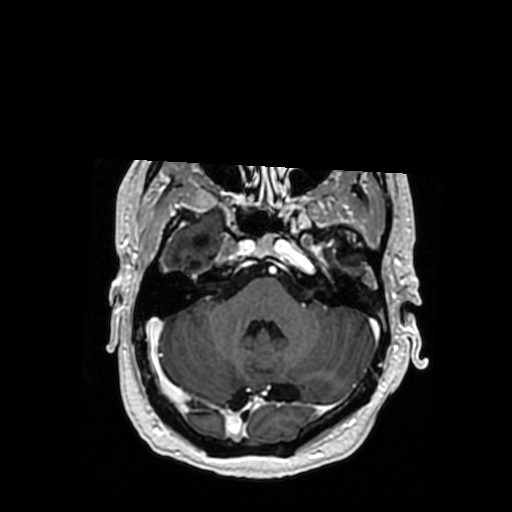
Brain MRI from a brain-tumour surgery series, one axial slice; T1-weighted post-contrast; 512 × 512 image matrix, field of view 260 × 260 mm. From the clinical record (not read from this slice): histopathology: Oligodendroglioma; WHO grade: 3; IDH mutation: yes; tumour location: Right Posterior Temporal Inferior Parietal.
Annotated regions visible in this slice (outlined manually by an expert reader):
- previous resection cavity: bounding box (x1, y1, x2, y2) in pixels: (190, 234, 210, 270)